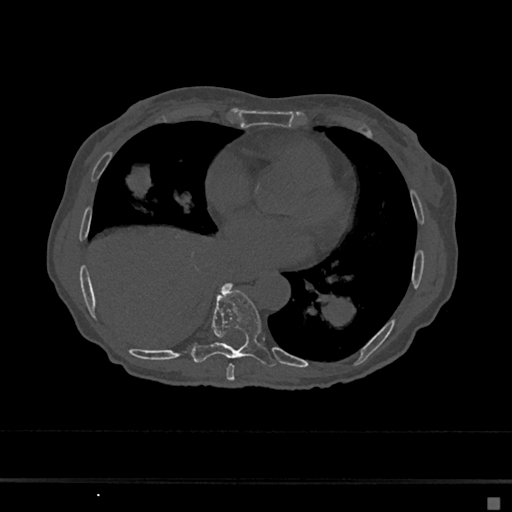
CT including the spine, one axial slice. Reconstruction kernel Br40s/3. 120 kVp. Bone window (W 1800 / L 400 HU). 512 × 512 image matrix, field of view 360 × 360 mm. Patient: female, 68 years. From the clinical record (not read from this slice): primary cancer: renal.
Annotated regions visible in this slice (semi-automatic segmentation, software-assisted and operator-edited):
- T7 vertebra: bounding box [x1, y1, x2, y2] px = [226, 364, 235, 381]
- T8 vertebra: [191, 283, 276, 367]